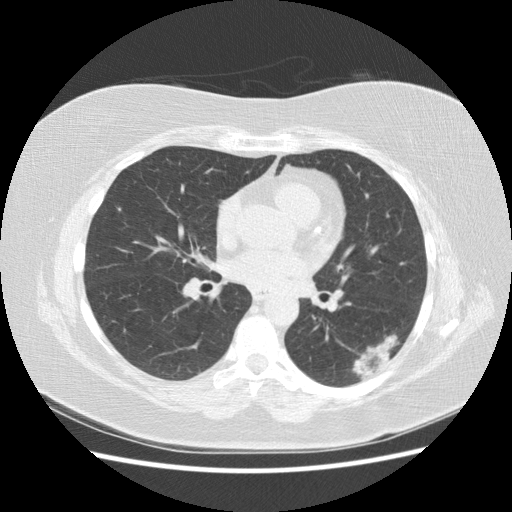
Chest CT (low-dose screening protocol), one axial image, third screening round (two years after baseline), lung window (W 1500 / L -600 HU), 2.5 mm slice thickness, slice 78 of 151 in the series, 512 × 512 image matrix. Female participant, aged 57 years at enrolment. Current smoker at enrolment.
- Expert-annotated lung lesion, bounding box <335,324,408,388> (left, top, right, bottom; pixels).
- Reader record for this screening exam (exam-level; its link to the box is not recorded): non-calcified nodule or mass ≥4 mm, left lower lobe, 40 × 20 mm, poorly defined margins, mixed attenuation, pre-existing on the prior screen: yes; interval growth: yes.